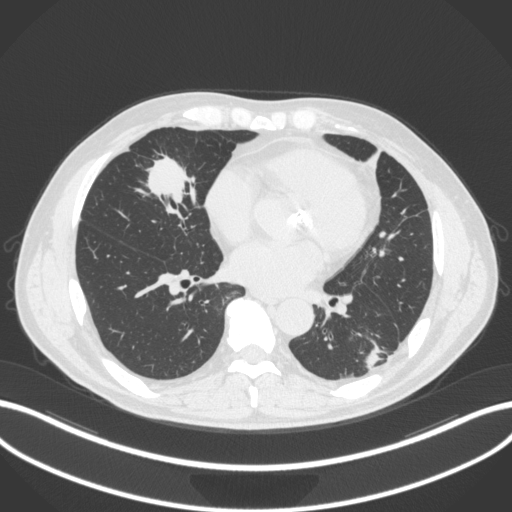
Chest CT, one axial slice. Position 121 of 399 along the scan axis. Lung window (W 1500 / L -600 HU). 512 × 512 image matrix. Male patient, age 59 years. From the clinical record (not read from this slice): clinical TNM (as recorded): T2a N1 M0.
Structures marked on this image (bounding box drawn by a radiologist):
- lung tumour (recorded histology: adenocarcinoma): bounding box <131,151,207,221> (left, top, right, bottom; pixels)